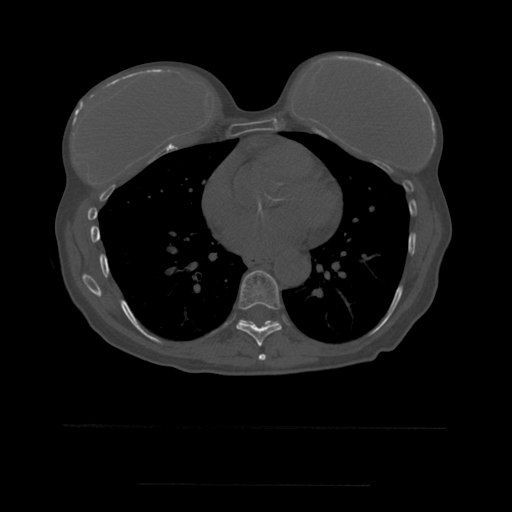
CT including the spine, one axial slice; slice 336 of 544 in the series (ordered by position); bone window (W 1800 / L 400 HU); 1.25 mm slice thickness; 512 × 512 image matrix. Patient age 58 years. From the clinical record (not read from this slice): primary cancer: lung.
Structures marked on this image (semi-automatic segmentation, software-assisted and operator-edited):
- T7 vertebra: bounding box <258,354,266,361> (left, top, right, bottom; pixels)
- T8 vertebra: <236,270,282,347>
- T9 vertebra: <240,320,279,323>